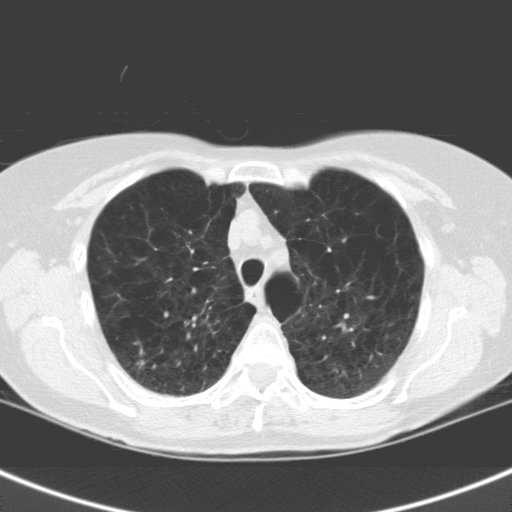
Chest CT (low-dose screening protocol), one axial image. Second annual screen. Lung window (W 1500 / L -600 HU). 3.2 mm slice thickness. Standard (soft-tissue) reconstruction kernel (C). 120 kVp. 512 × 512 image matrix, field of view 301 × 301 mm. Female, age 63 years at enrolment.
Expert reader's lesion annotation, bounding box [x1, y1, x2, y2] px = [111, 338, 162, 388]. Reader record for this screening exam (exam-level; its link to the box is not recorded): non-calcified nodule or mass ≥4 mm, right upper lobe, 7 × 7 mm, spiculated (stellate) margins, soft tissue attenuation, pre-existing on the prior screen: no.